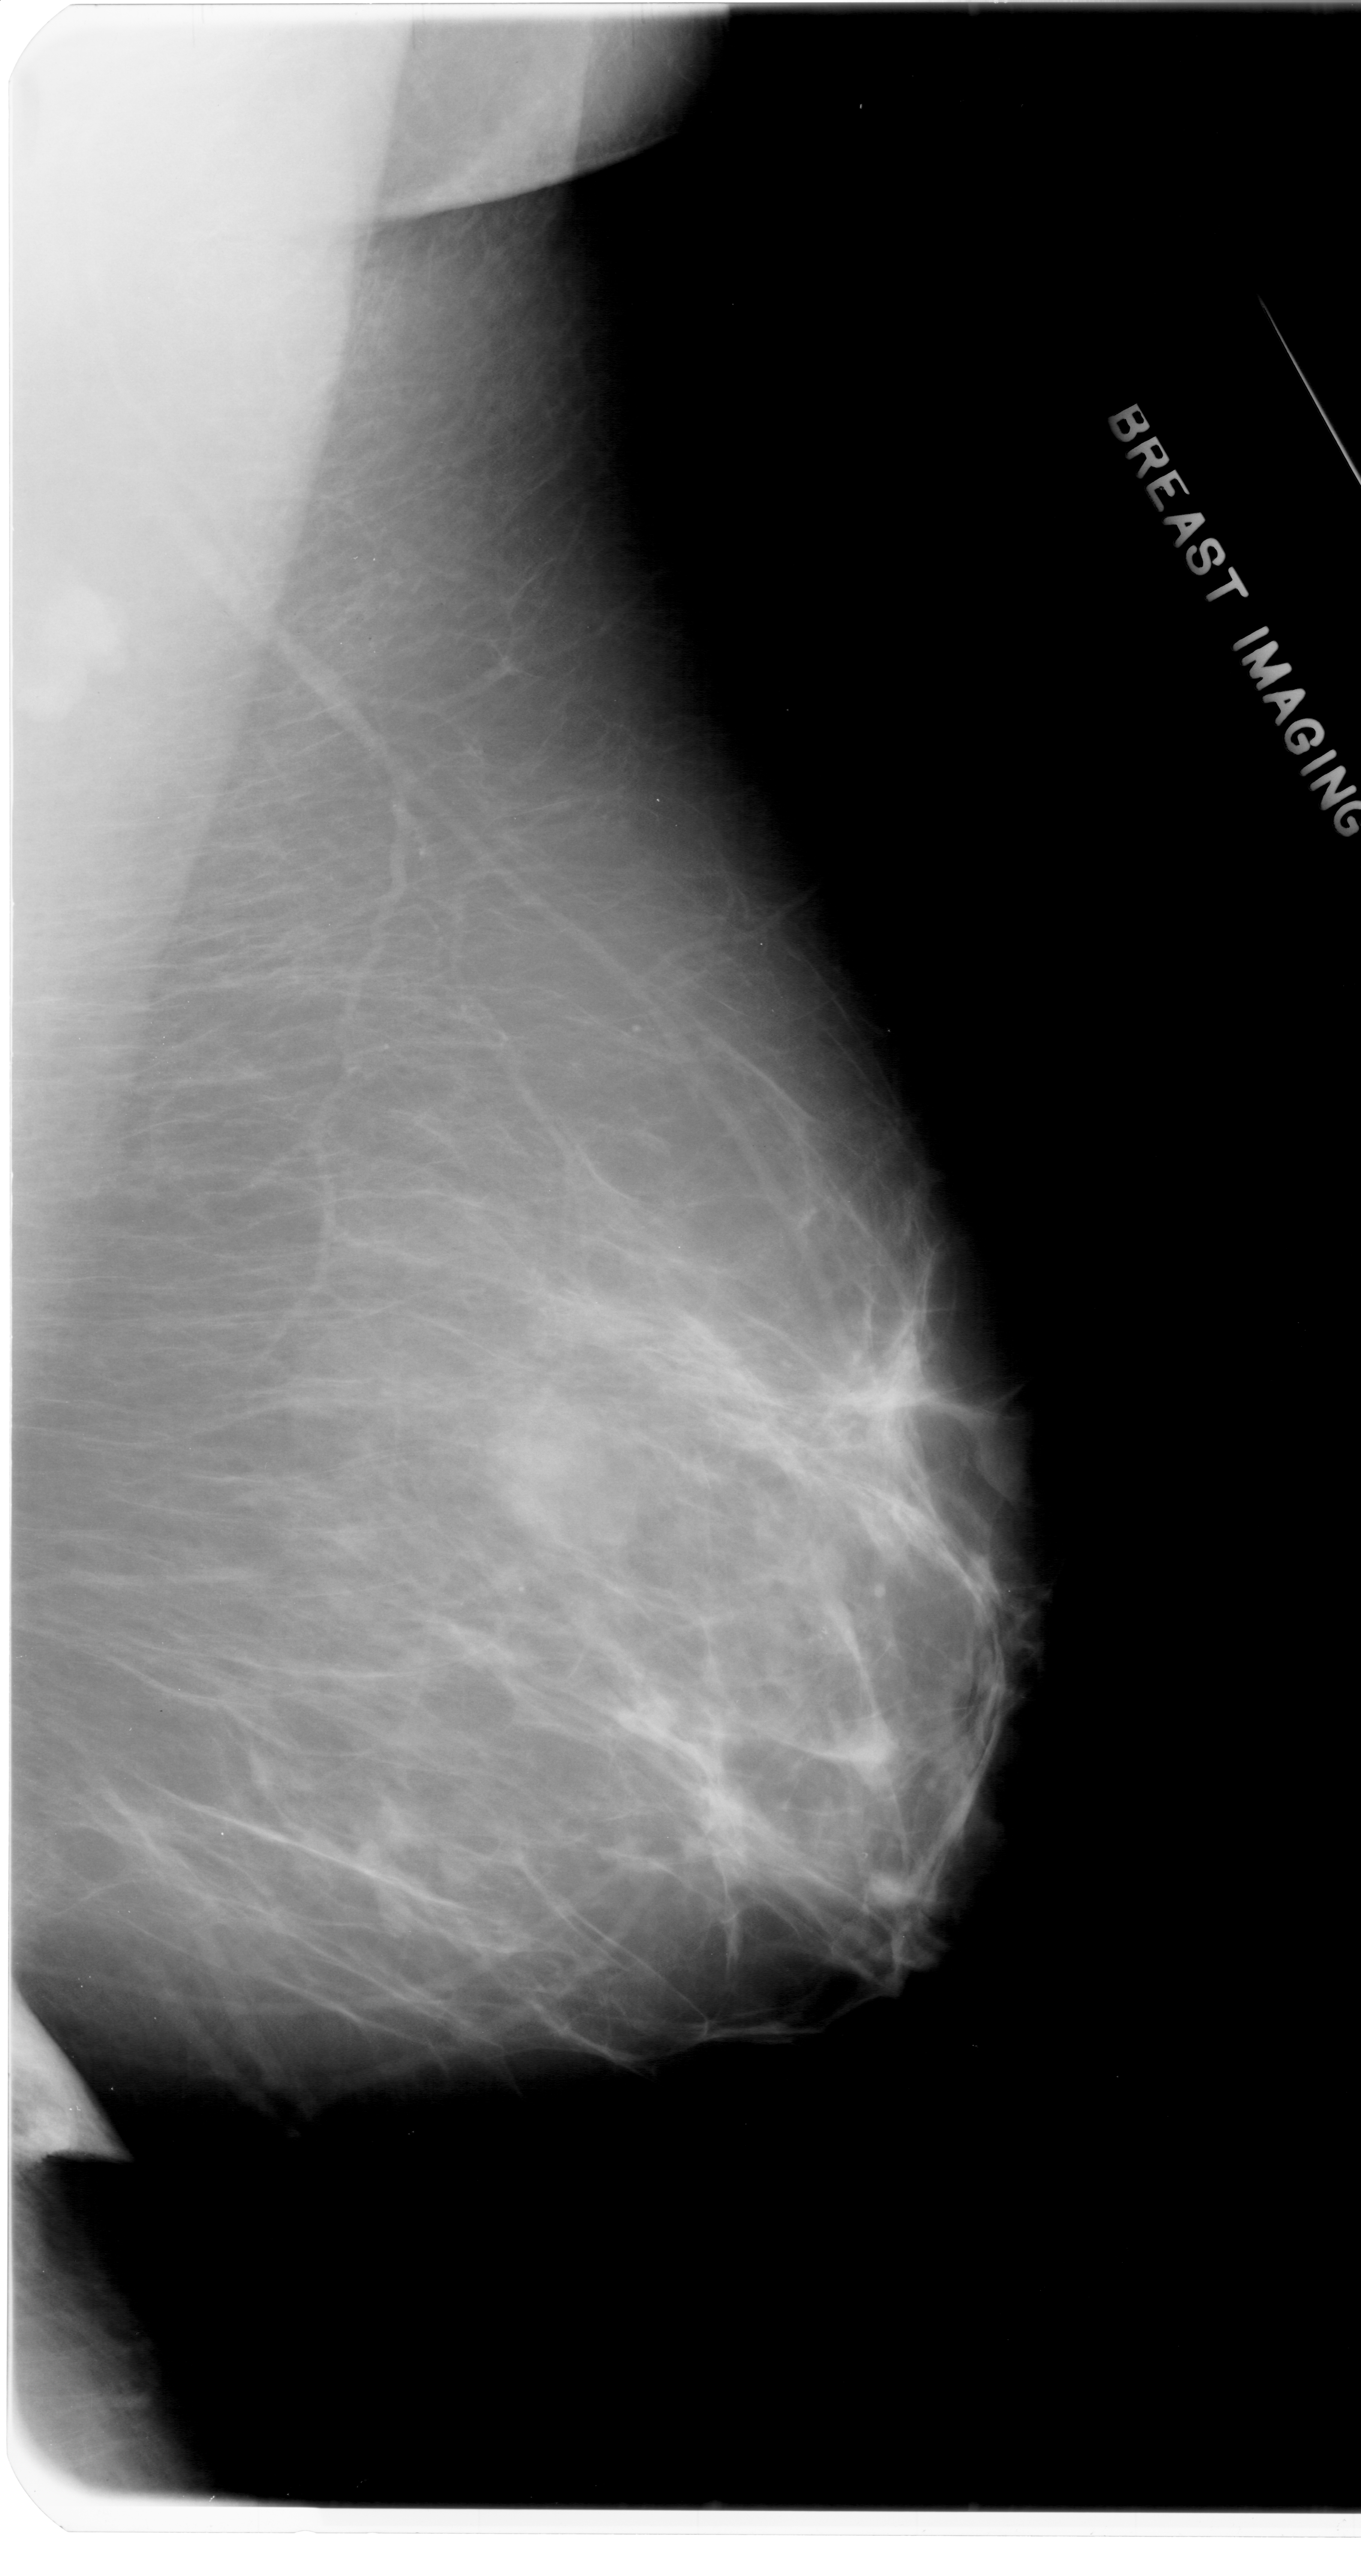
Digitized screen-film mammogram, right breast, mediolateral oblique (MLO) view, BI-RADS breast density category 2 (scale 1–4).
Abnormality record for this image: calcifications, morphology pleomorphic, distribution clustered; BI-RADS assessment category 4; pathology (as recorded): benign.